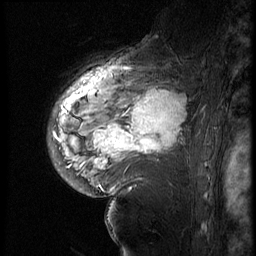
Breast MRI (dynamic contrast-enhanced), one sagittal slice. Position 44 of 60 along the scan axis. 4 images stored at this slice position (order not interpretable as contrast timing). 1.5 T. TE 4.2 ms, TR 9 ms. 256 × 256 image matrix, field of view 180 × 180 mm. Female patient, age 56 years. Case-level facts recorded for this patient, not image findings: setting: breast cancer imaged before/during neoadjuvant chemotherapy; receptor status: HER2-positive.
Outlined on this slice (semi-automatically segmented with operator editing):
- analysis volume of interest (the breast-tissue region the enhancement analysis was run in; not a lesion): bounding box <82,83,199,177> (left, top, right, bottom; pixels)
- tumour enhancement mask (voxels above the 140 % enhancement threshold inside the analysis volume of interest): <95,90,187,167>